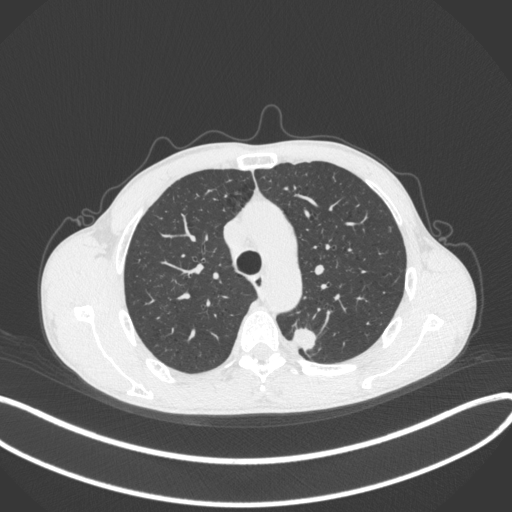
Chest CT, one axial slice; position 288 of 429 along the scan axis; reconstruction kernel B31f; 120 kVp; lung window (W 1500 / L -600 HU); 512 × 512 image matrix, field of view 400 × 400 mm. Male patient, age 51 years. Case-level facts recorded for this patient, not image findings: clinical TNM (as recorded): T2a N1 M1.
Structures marked on this image (bounding box drawn by a radiologist):
- lung tumour (recorded histology: adenocarcinoma): bounding box (x1, y1, x2, y2) in pixels: (290, 325, 318, 356)